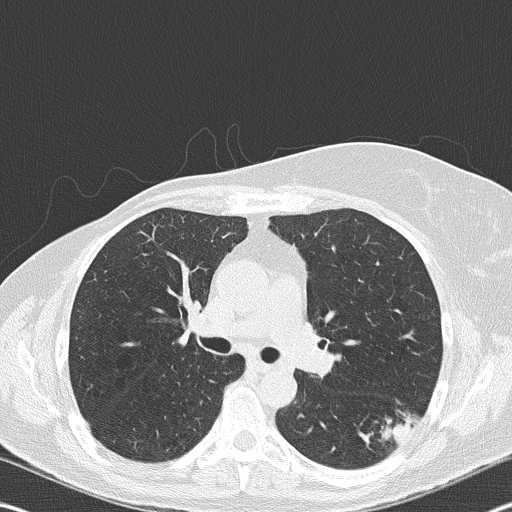
Low-dose screening chest CT, axial slice; second annual screen; lung window (W 1500 / L -600 HU); 2 mm slice thickness; slice 112 of 177 in the series. Female, age 60 years at enrolment. Current smoker at enrolment.
Expert reader's lesion annotation, bounding box (x1, y1, x2, y2) in pixels: (364, 389, 429, 449). Reader record for this screening exam (exam-level; its link to the box is not recorded): non-calcified nodule or mass ≥4 mm, left lower lobe, 18 × 16 mm, spiculated (stellate) margins, soft tissue attenuation, pre-existing on the prior screen: no. Later outcome: lung cancer diagnosed 35 days after this screen — carcinoma, NOS, left hilum, stage IV (AJCC 6th edition), 45 mm at pathology.